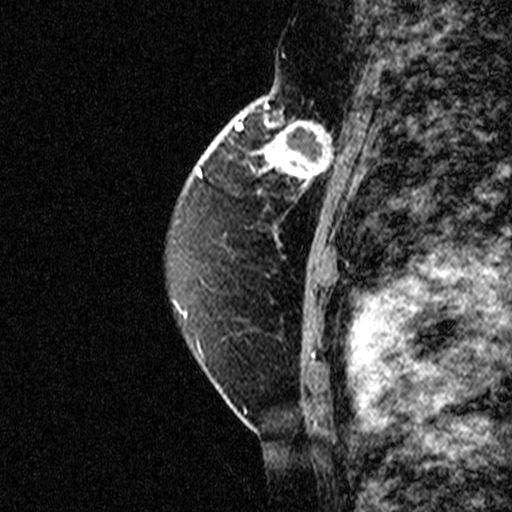
Breast MRI (dynamic contrast-enhanced), one sagittal slice. Position 28 of 44 along the scan axis. Dynamic contrast-enhanced study with each time point stored as its own series, time point 2 of 3 at this slice position (early post-contrast, ordered by acquisition time). 1.5 T. TE 4.5 ms, TR 11 ms. 512 × 512 image matrix. Female patient, age 49 years. Case-level facts recorded for this patient, not image findings: setting: breast cancer imaged before/during neoadjuvant chemotherapy; receptor status: triple-negative.
Structures marked on this image (semi-automatic segmentation, software-assisted and operator-edited):
- analysis volume of interest (the breast-tissue region the enhancement analysis was run in; not a lesion): bounding box <254,112,347,207> (left, top, right, bottom; pixels)
- tumour enhancement mask (voxels above the 90 % enhancement threshold inside the analysis volume of interest): <254,112,347,207>